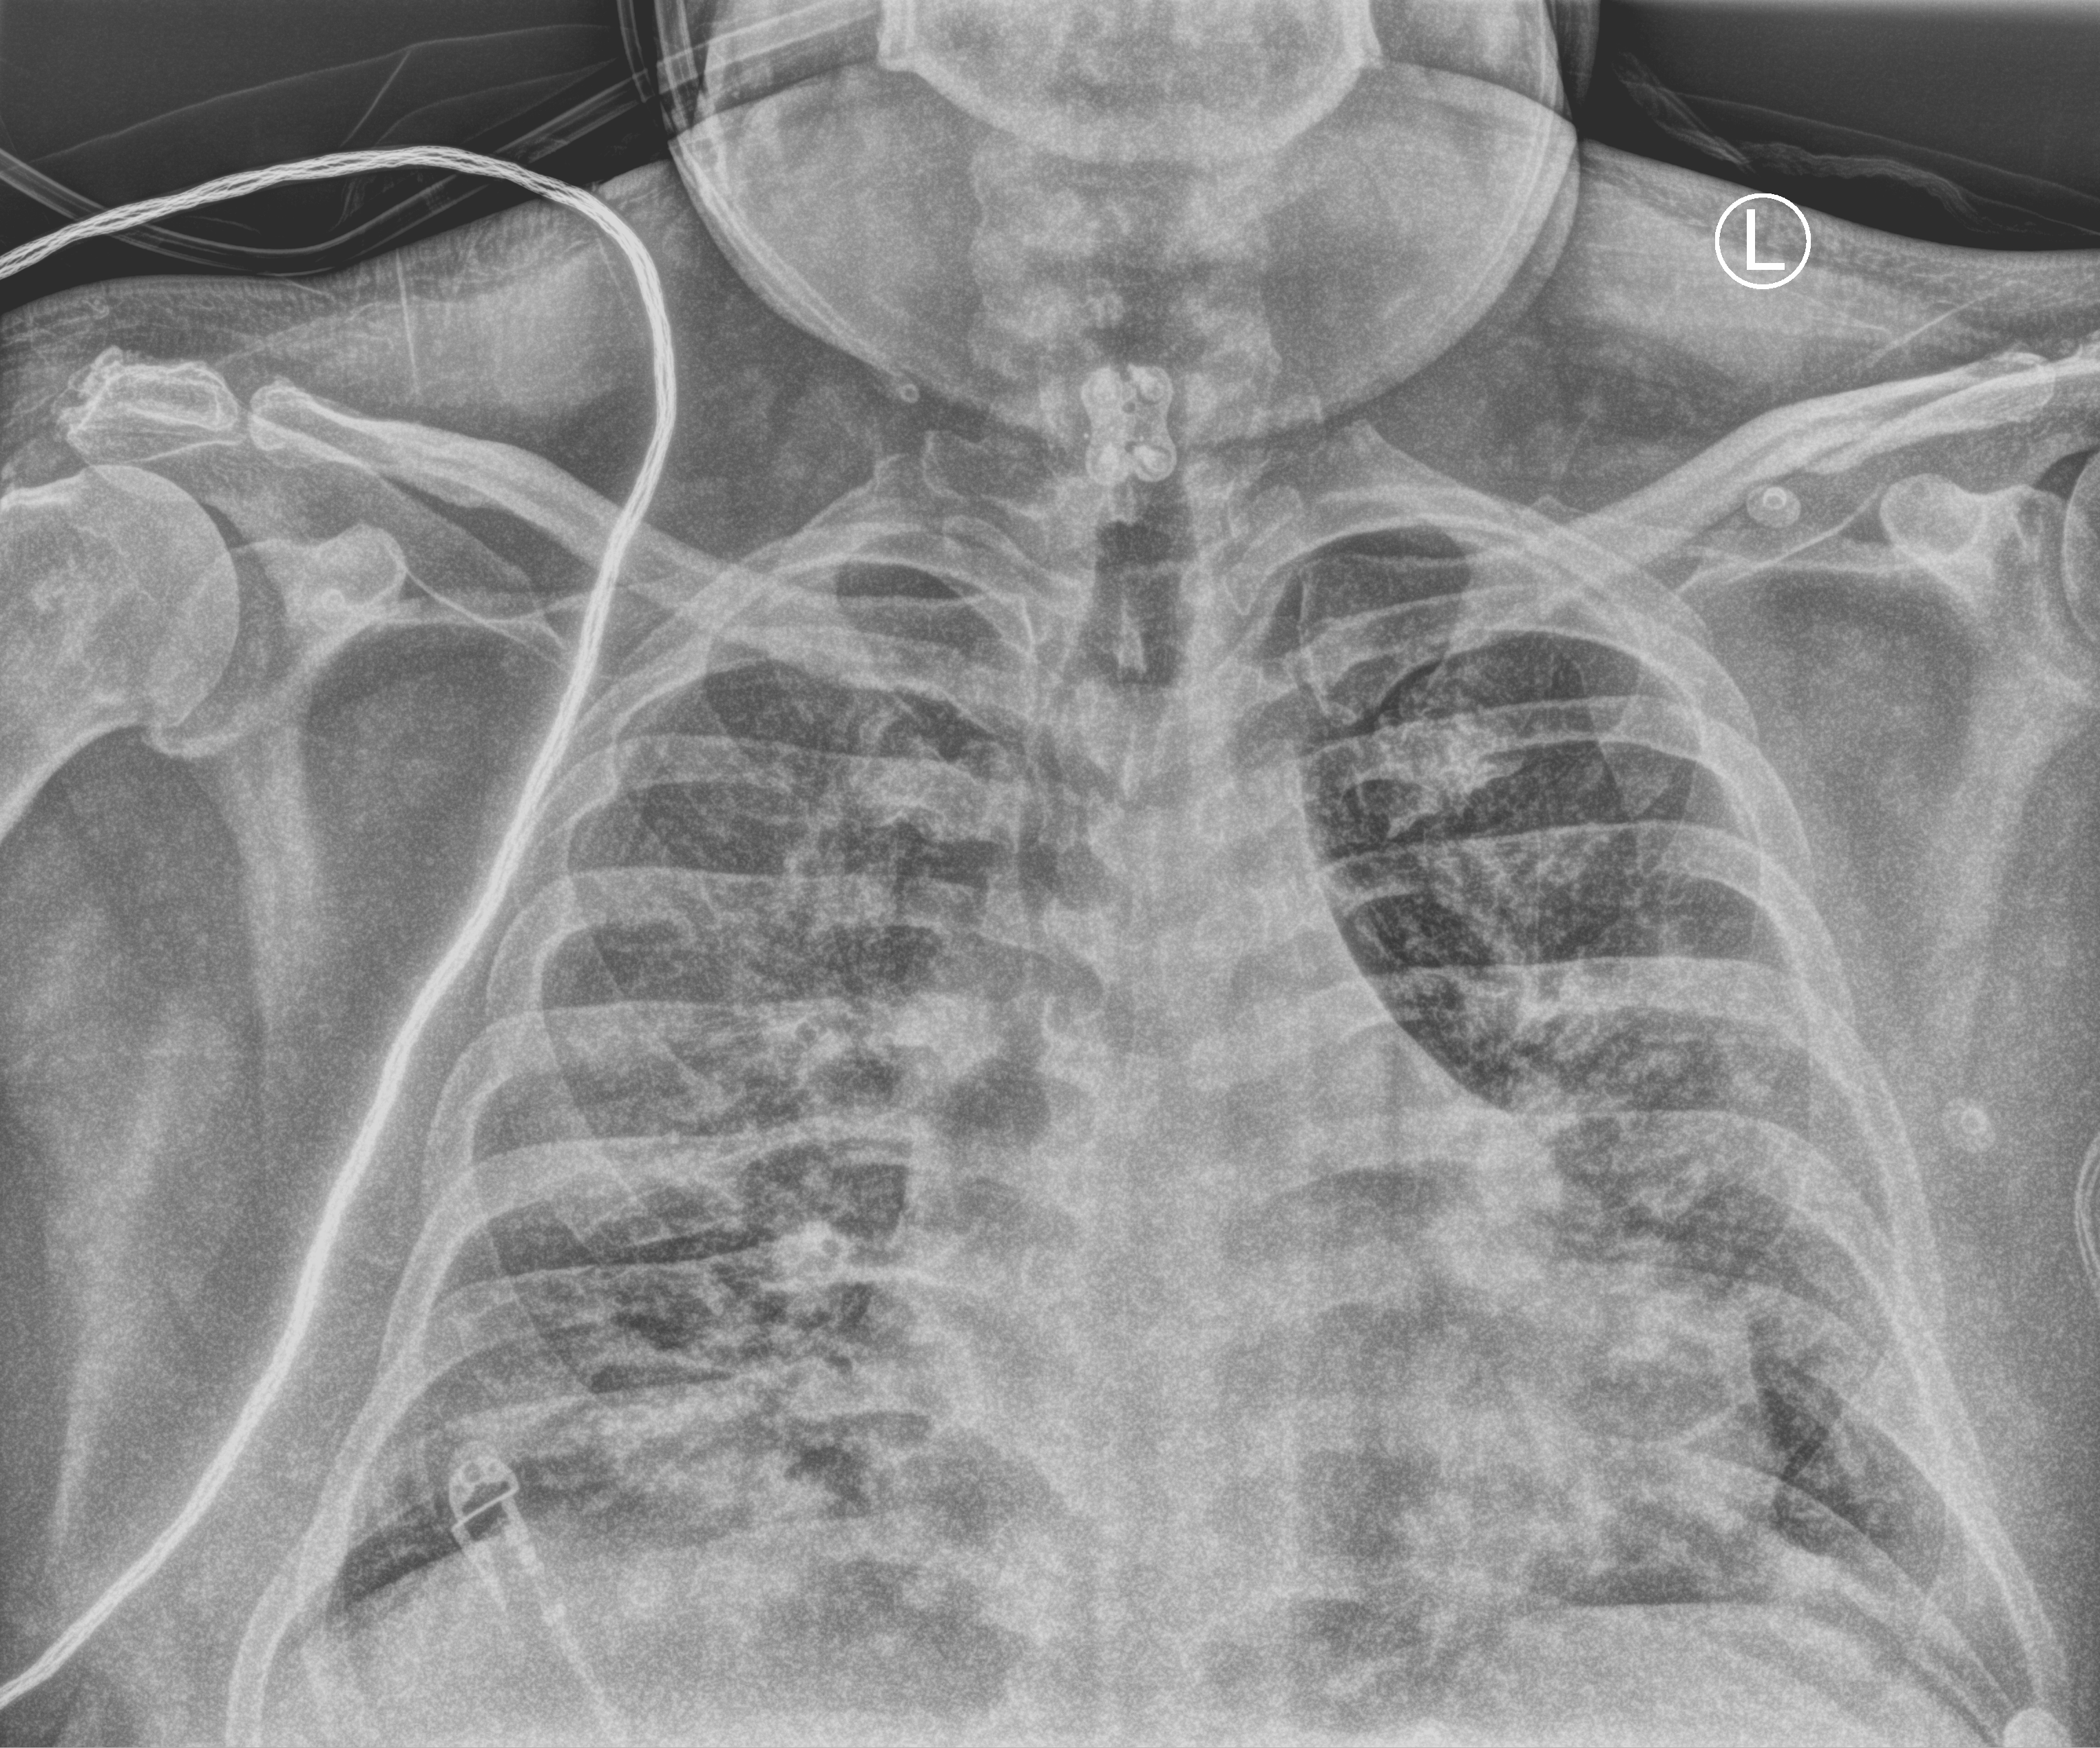
Chest X-ray (portable), anteroposterior (AP) projection. Male patient hospitalised with COVID-19, age 18–59 years.
Admission-level facts for this patient (not findings on this image; timing relative to this image not recorded):
- mechanically ventilated during this hospital stay: yes